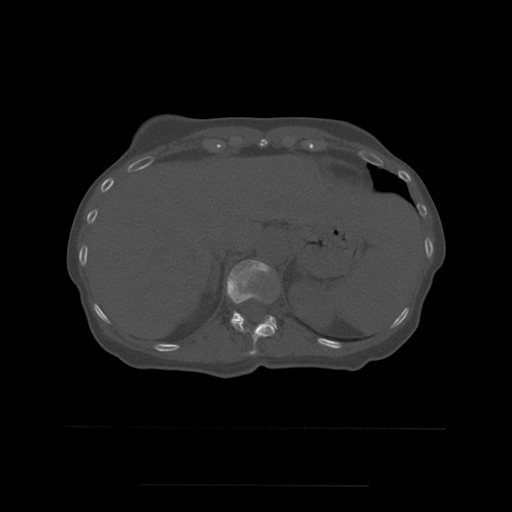
CT including the spine, one axial slice. Slice 271 of 544 in the series (ordered by position). Bone window (W 1800 / L 400 HU). 1.25 mm slice thickness. 512 × 512 image matrix, field of view 350 × 350 mm. Patient age 58 years. Case-level facts recorded for this patient, not image findings: primary cancer: lung.
Annotated regions visible in this slice (semi-automatically segmented with operator editing):
- T11 vertebra: bounding box (x1, y1, x2, y2) in pixels: (231, 296, 275, 355)
- T12 vertebra: (227, 260, 278, 331)